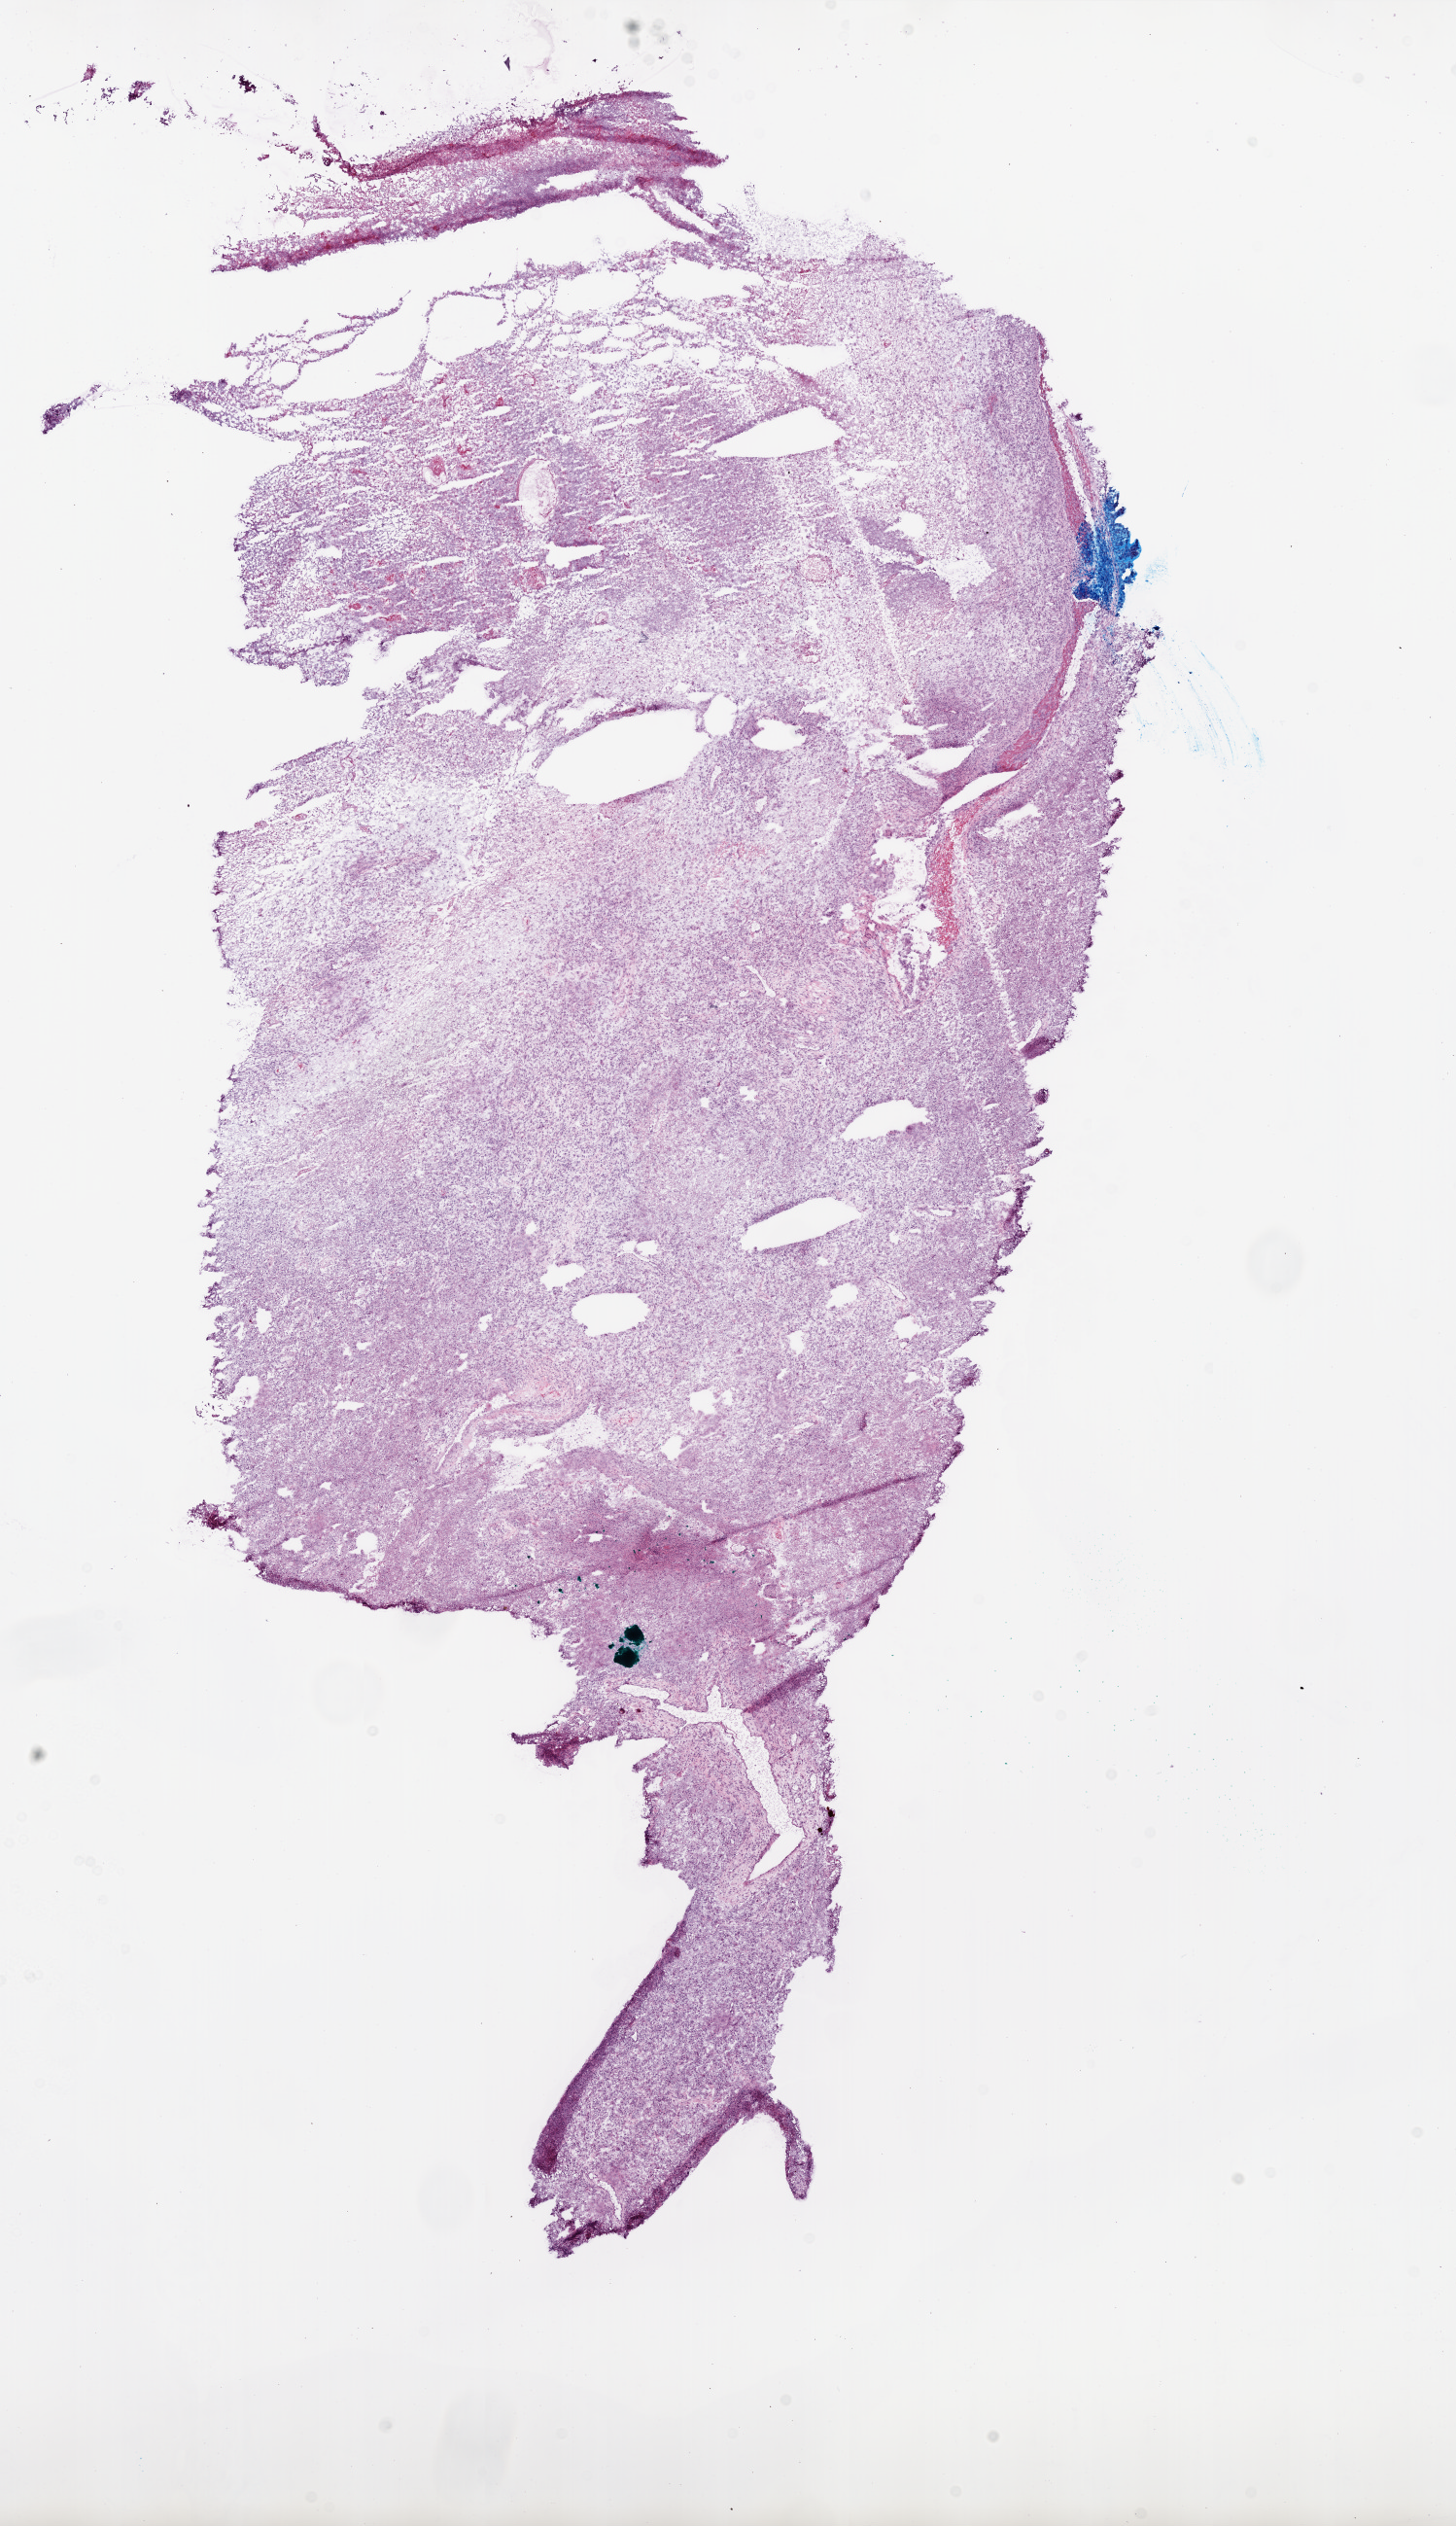
Whole-slide histology image, H&E-stained, shown as a low-resolution overview of the whole scanned area (about 12.0 x 20.8 mm, acquisition: 20x scan). Frozen section. Sample: primary tumour, brain. Male, age 50 years at initial diagnosis. Slide review estimates, as recorded: tumour cells 70%, tumour nuclei 95%, normal cells 0%, stromal cells 0%, necrosis 30%.
Histologic diagnosis: Glioblastoma.